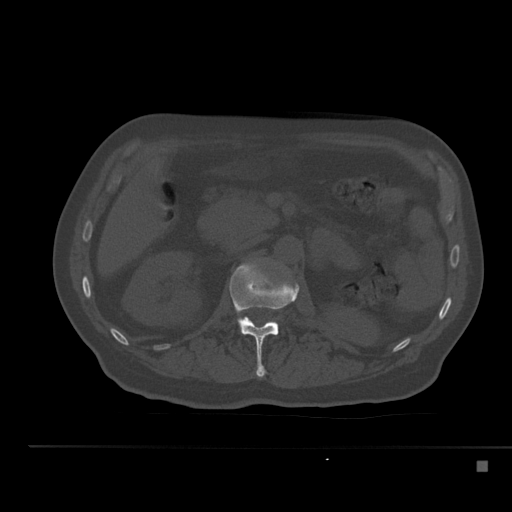
CT including the spine, one axial slice. Position 204 of 517 along the scan axis. Reconstruction kernel Br40s. 120 kVp. Bone window (W 1800 / L 400 HU). 1.5 mm slice thickness. 512 × 512 image matrix, field of view 408 × 408 mm. Male patient, age 70 years. From the clinical record (not read from this slice): primary cancer: renal; vertebrae with lytic lesions (as recorded): T4, T6, T10, T12, L3, L4, L5.
Annotated regions visible in this slice (semi-automatic segmentation, software-assisted and operator-edited):
- L1 vertebra: box from (x=229, y=260) to (x=299, y=378) px